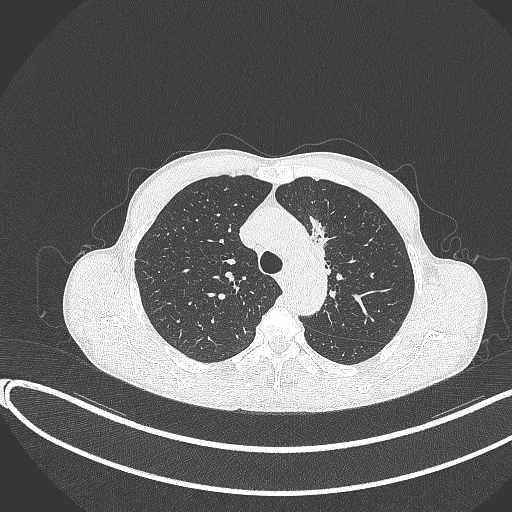
Chest CT, one axial slice; slice 276 of 374 in the series (ordered by position); lung window (W 1500 / L -600 HU); 512 × 512 image matrix. Male patient, age 58 years. From the clinical record (not read from this slice): clinical TNM (as recorded): T1c N1 M0.
Outlined on this slice (rectangle marked by the reading radiologist):
- lung tumour (recorded histology: adenocarcinoma): bounding box <301,211,332,268> (left, top, right, bottom; pixels)